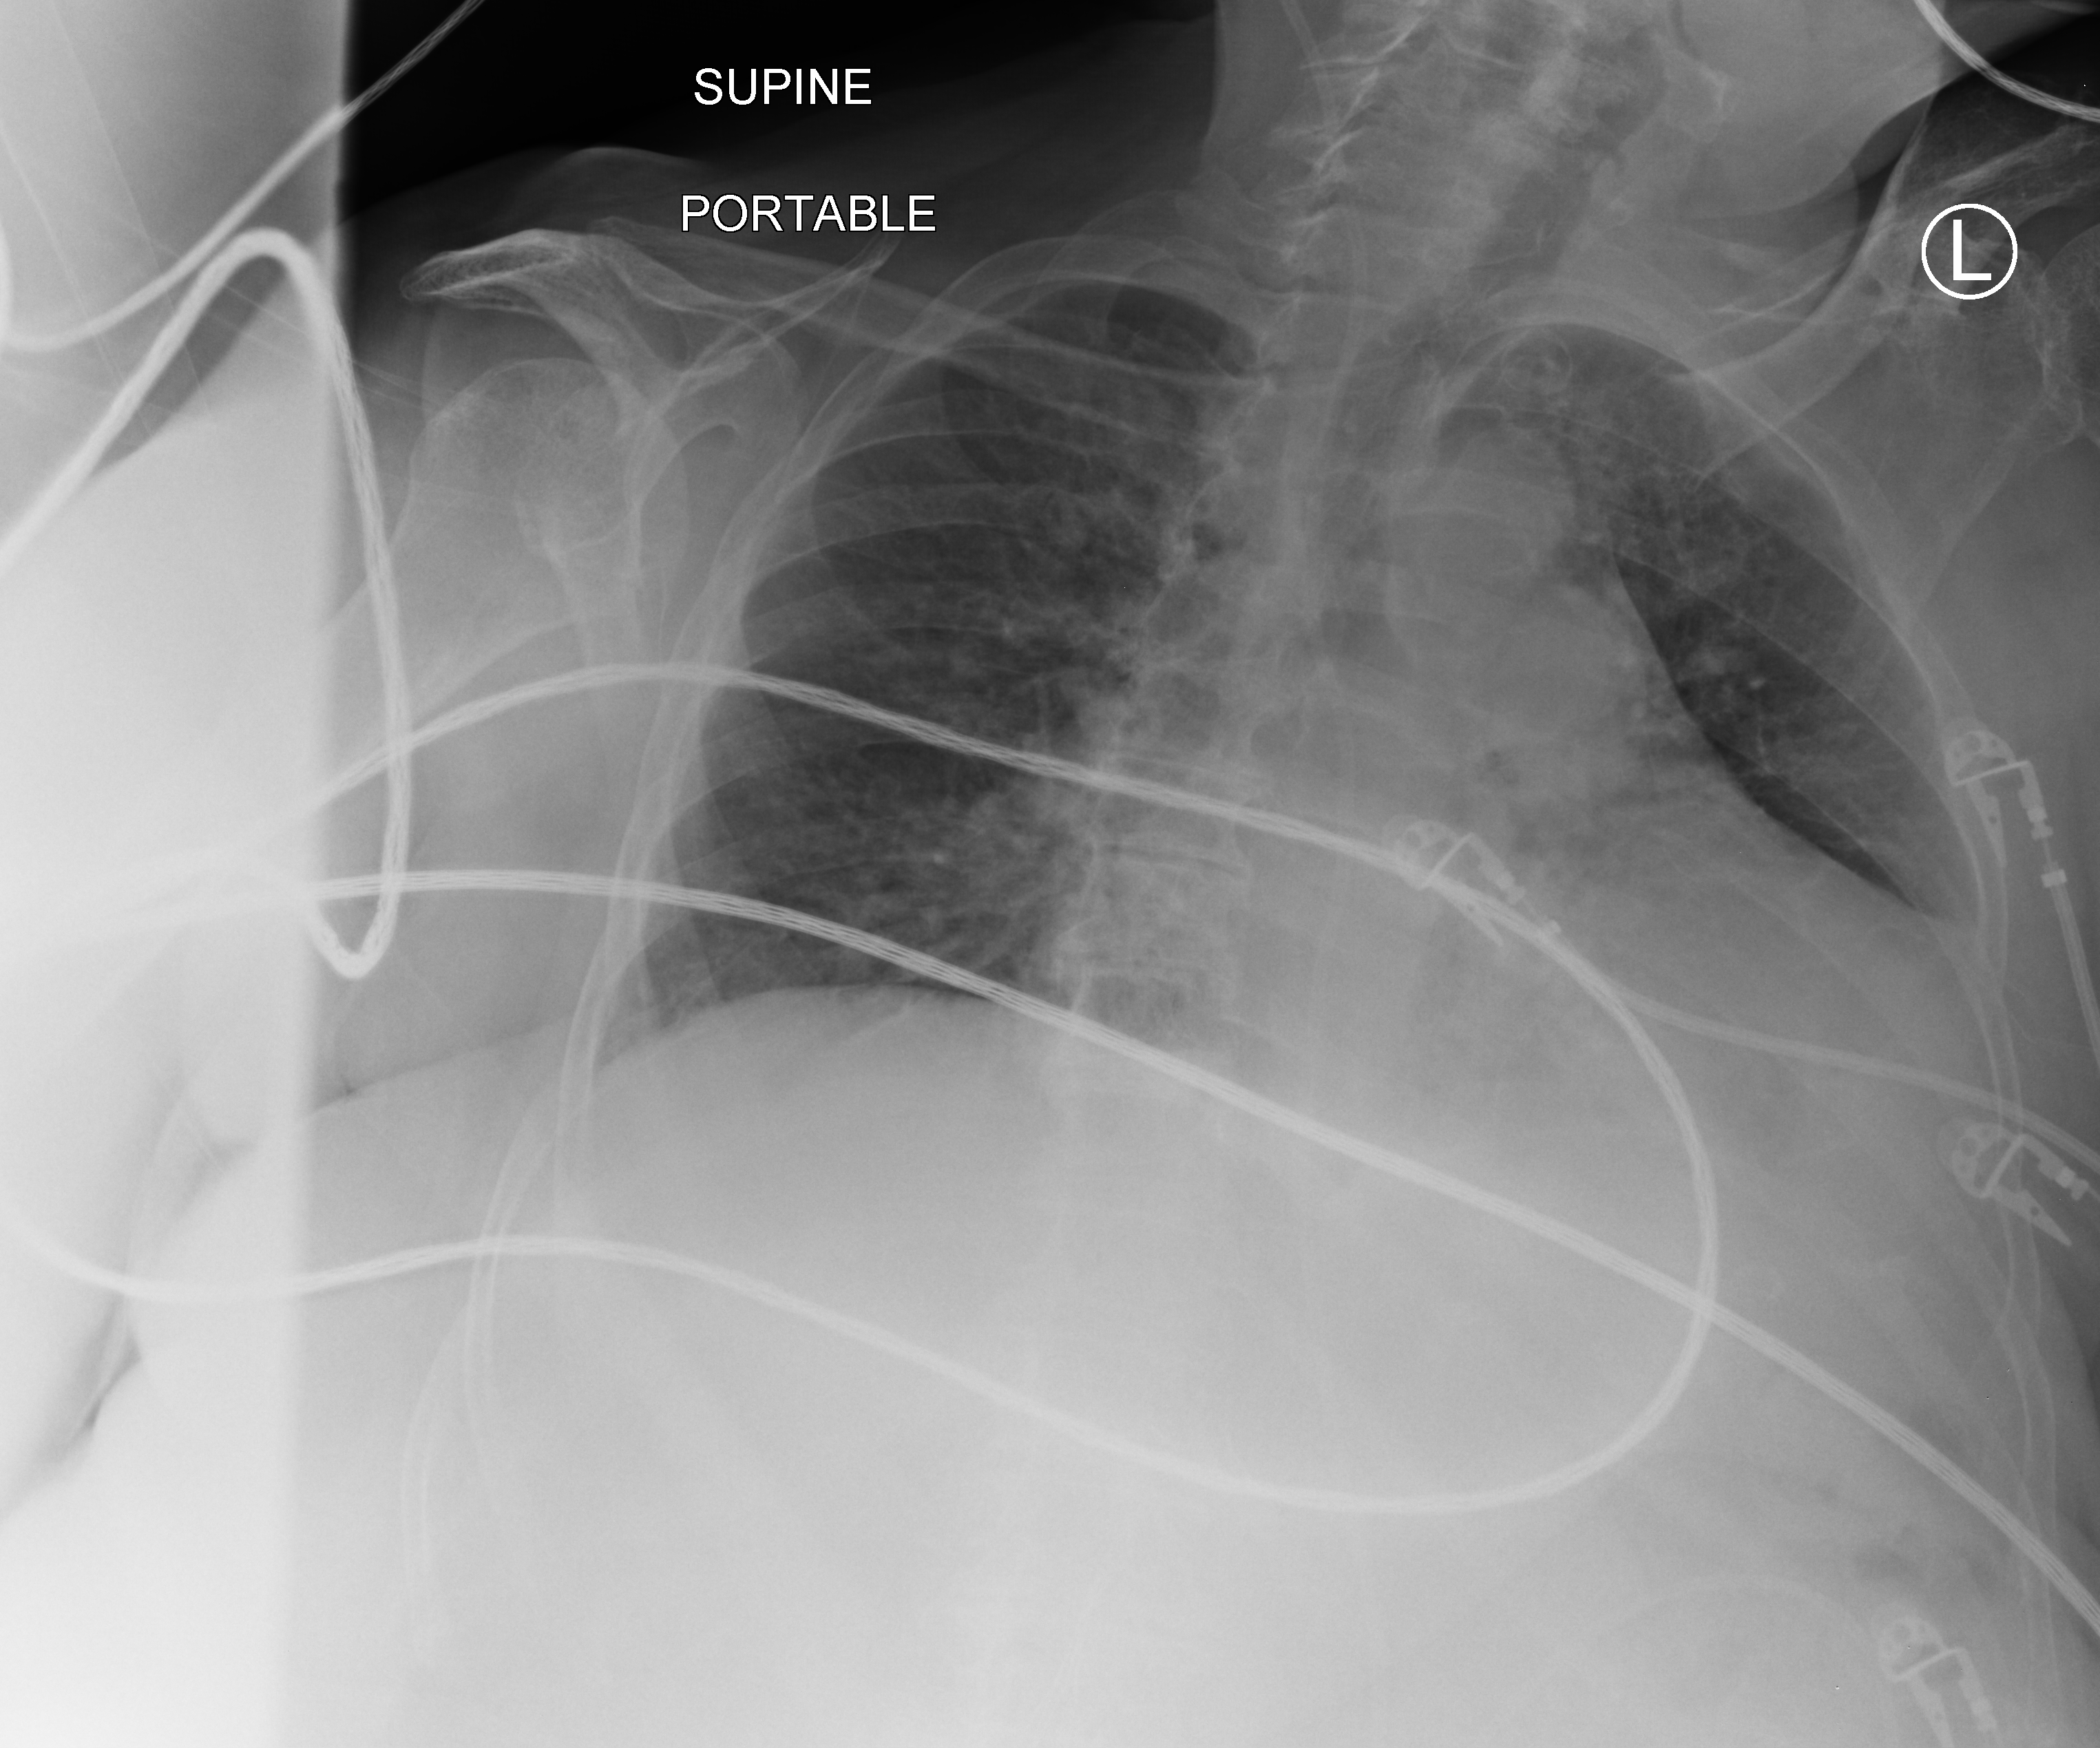
Chest X-ray (portable); anteroposterior (AP) projection. Female patient hospitalised with COVID-19, age 75–90 years.
Hospital-stay facts (about this admission, not read from this image; timing relative to this image not recorded):
- mechanically ventilated during this hospital stay: yes
- hypertension (admission record): yes